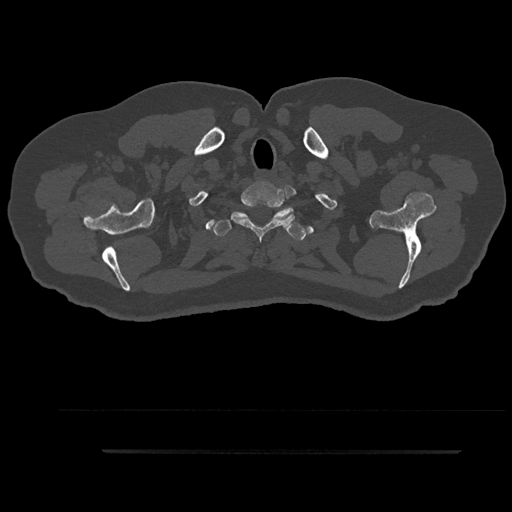
CT including the spine, one axial slice; slice 785 of 797 in the series (ordered by position); 120 kVp; bone window (W 1800 / L 400 HU); 0.5 mm slice thickness; 512 × 512 image matrix, field of view 432 × 432 mm. Male patient, age 63 years. Case-level facts recorded for this patient, not image findings: primary cancer: renal.
Outlined on this slice (semi-automatic segmentation, software-assisted and operator-edited):
- T1 vertebra: bounding box [x1, y1, x2, y2] px = [231, 185, 294, 241]
- T2 vertebra: [213, 206, 306, 241]